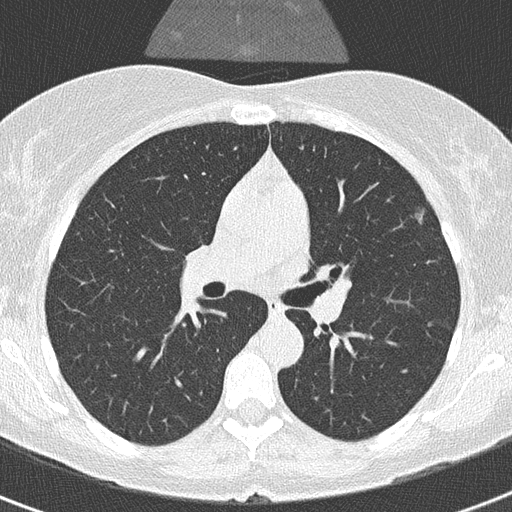
Low-dose screening chest CT, one axial slice; slice 201 of 320 in the series (ordered by position); 120 kVp; lung window (W 1500 / L -600 HU); 2 mm slice thickness; 512 × 512 image matrix.
Structures marked on this image (outlined manually by an expert reader):
- lesion 1 (tumor, upper lobe of left lung): bounding box <414,212,422,224> (left, top, right, bottom; pixels)